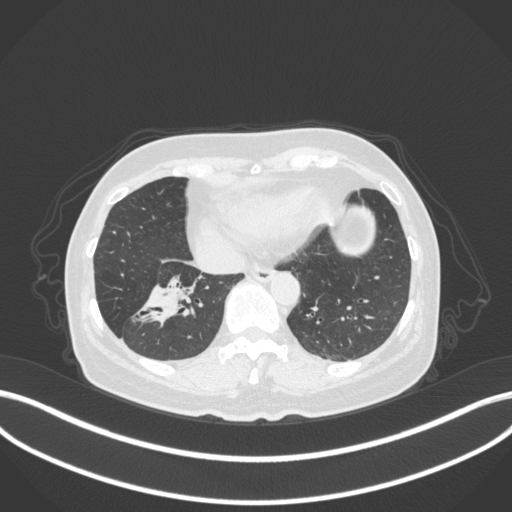
Chest CT, one axial slice; position 114 of 429 along the scan axis; 120 kVp; lung window (W 1500 / L -600 HU); 512 × 512 image matrix, field of view 400 × 400 mm. Female patient, age 67 years. From the clinical record (not read from this slice): clinical TNM (as recorded): T1c N1 M0.
Structures marked on this image (bounding box drawn by a radiologist):
- lung tumour (recorded histology: adenocarcinoma): bounding box (x1, y1, x2, y2) in pixels: (128, 270, 205, 331)